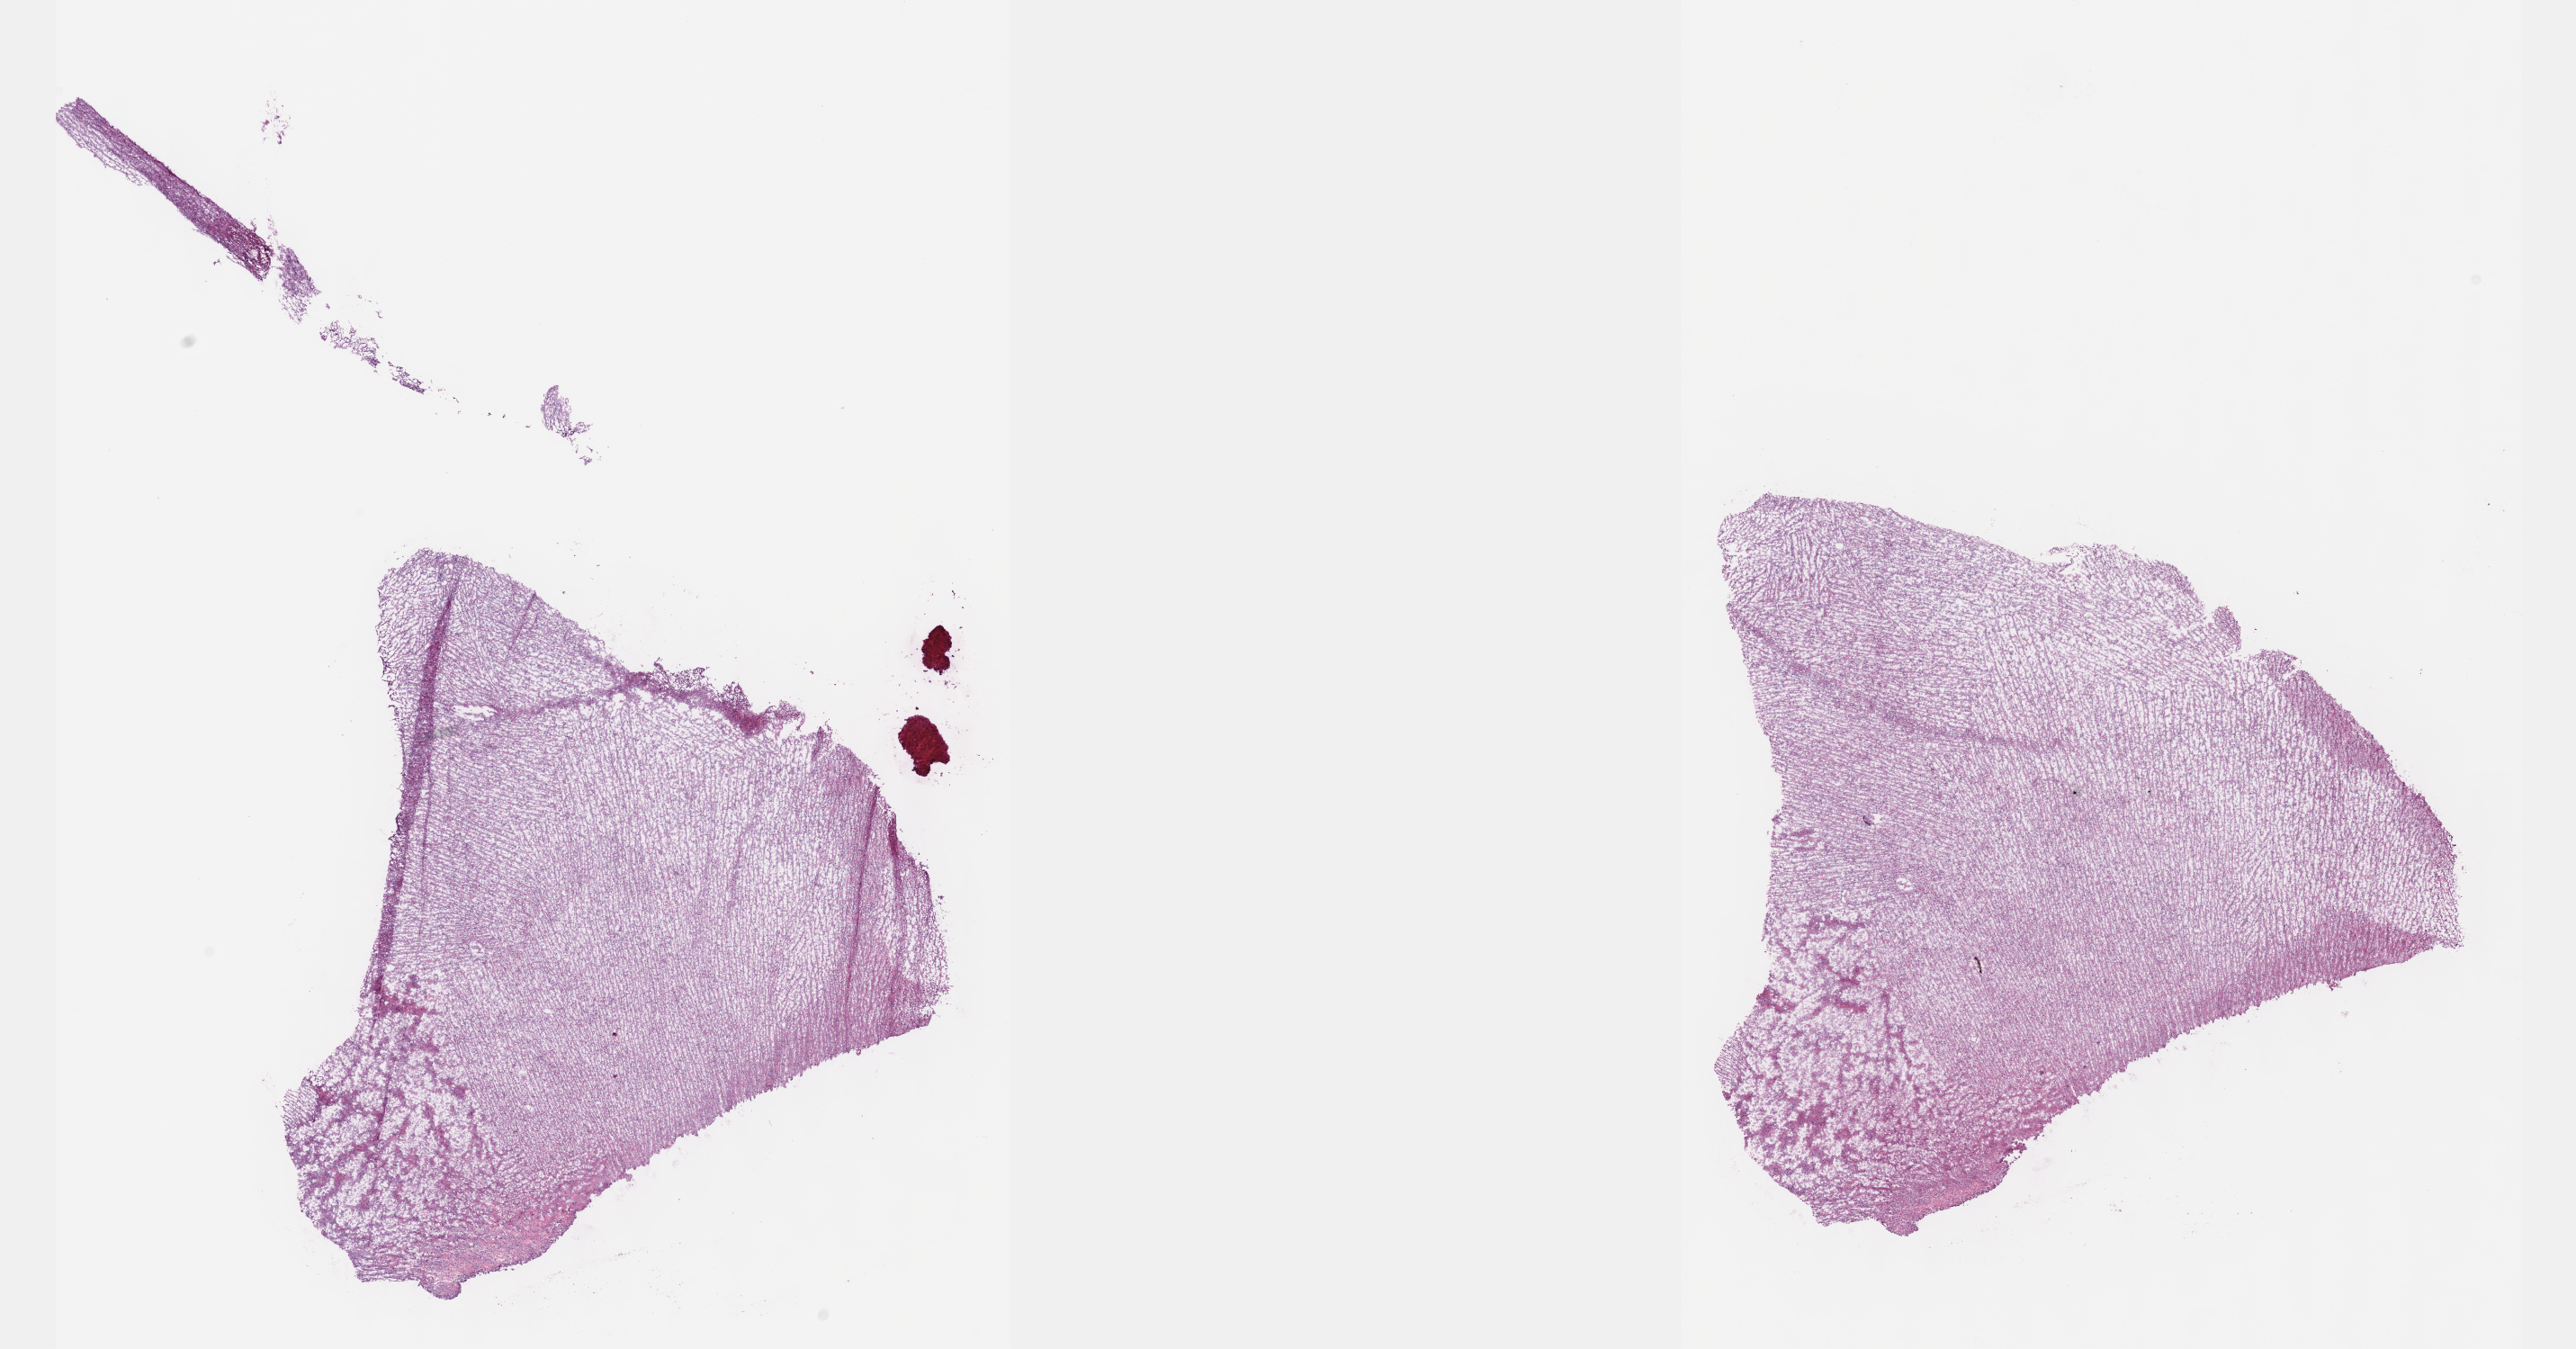
Whole-slide histology image, H&E — shown as a low-resolution overview of the whole scanned area (about 23.1 x 12.1 mm). Frozen section from the top of the tissue portion. Primary tumour sample from the brain. Female, age 37 years at initial diagnosis. Histologic grade: G2 (moderately differentiated). Pathologist review of this section (percent, as recorded): tumour cells 40%, tumour nuclei 90%, normal cells 10%, stromal cells 50%, necrosis 0%. Inflammatory infiltration, as recorded: lymphocyte infiltration 0%, monocyte infiltration 0%, neutrophil infiltration 0%.
Pathologic diagnosis: Oligodendroglioma, NOS (cerebrum).